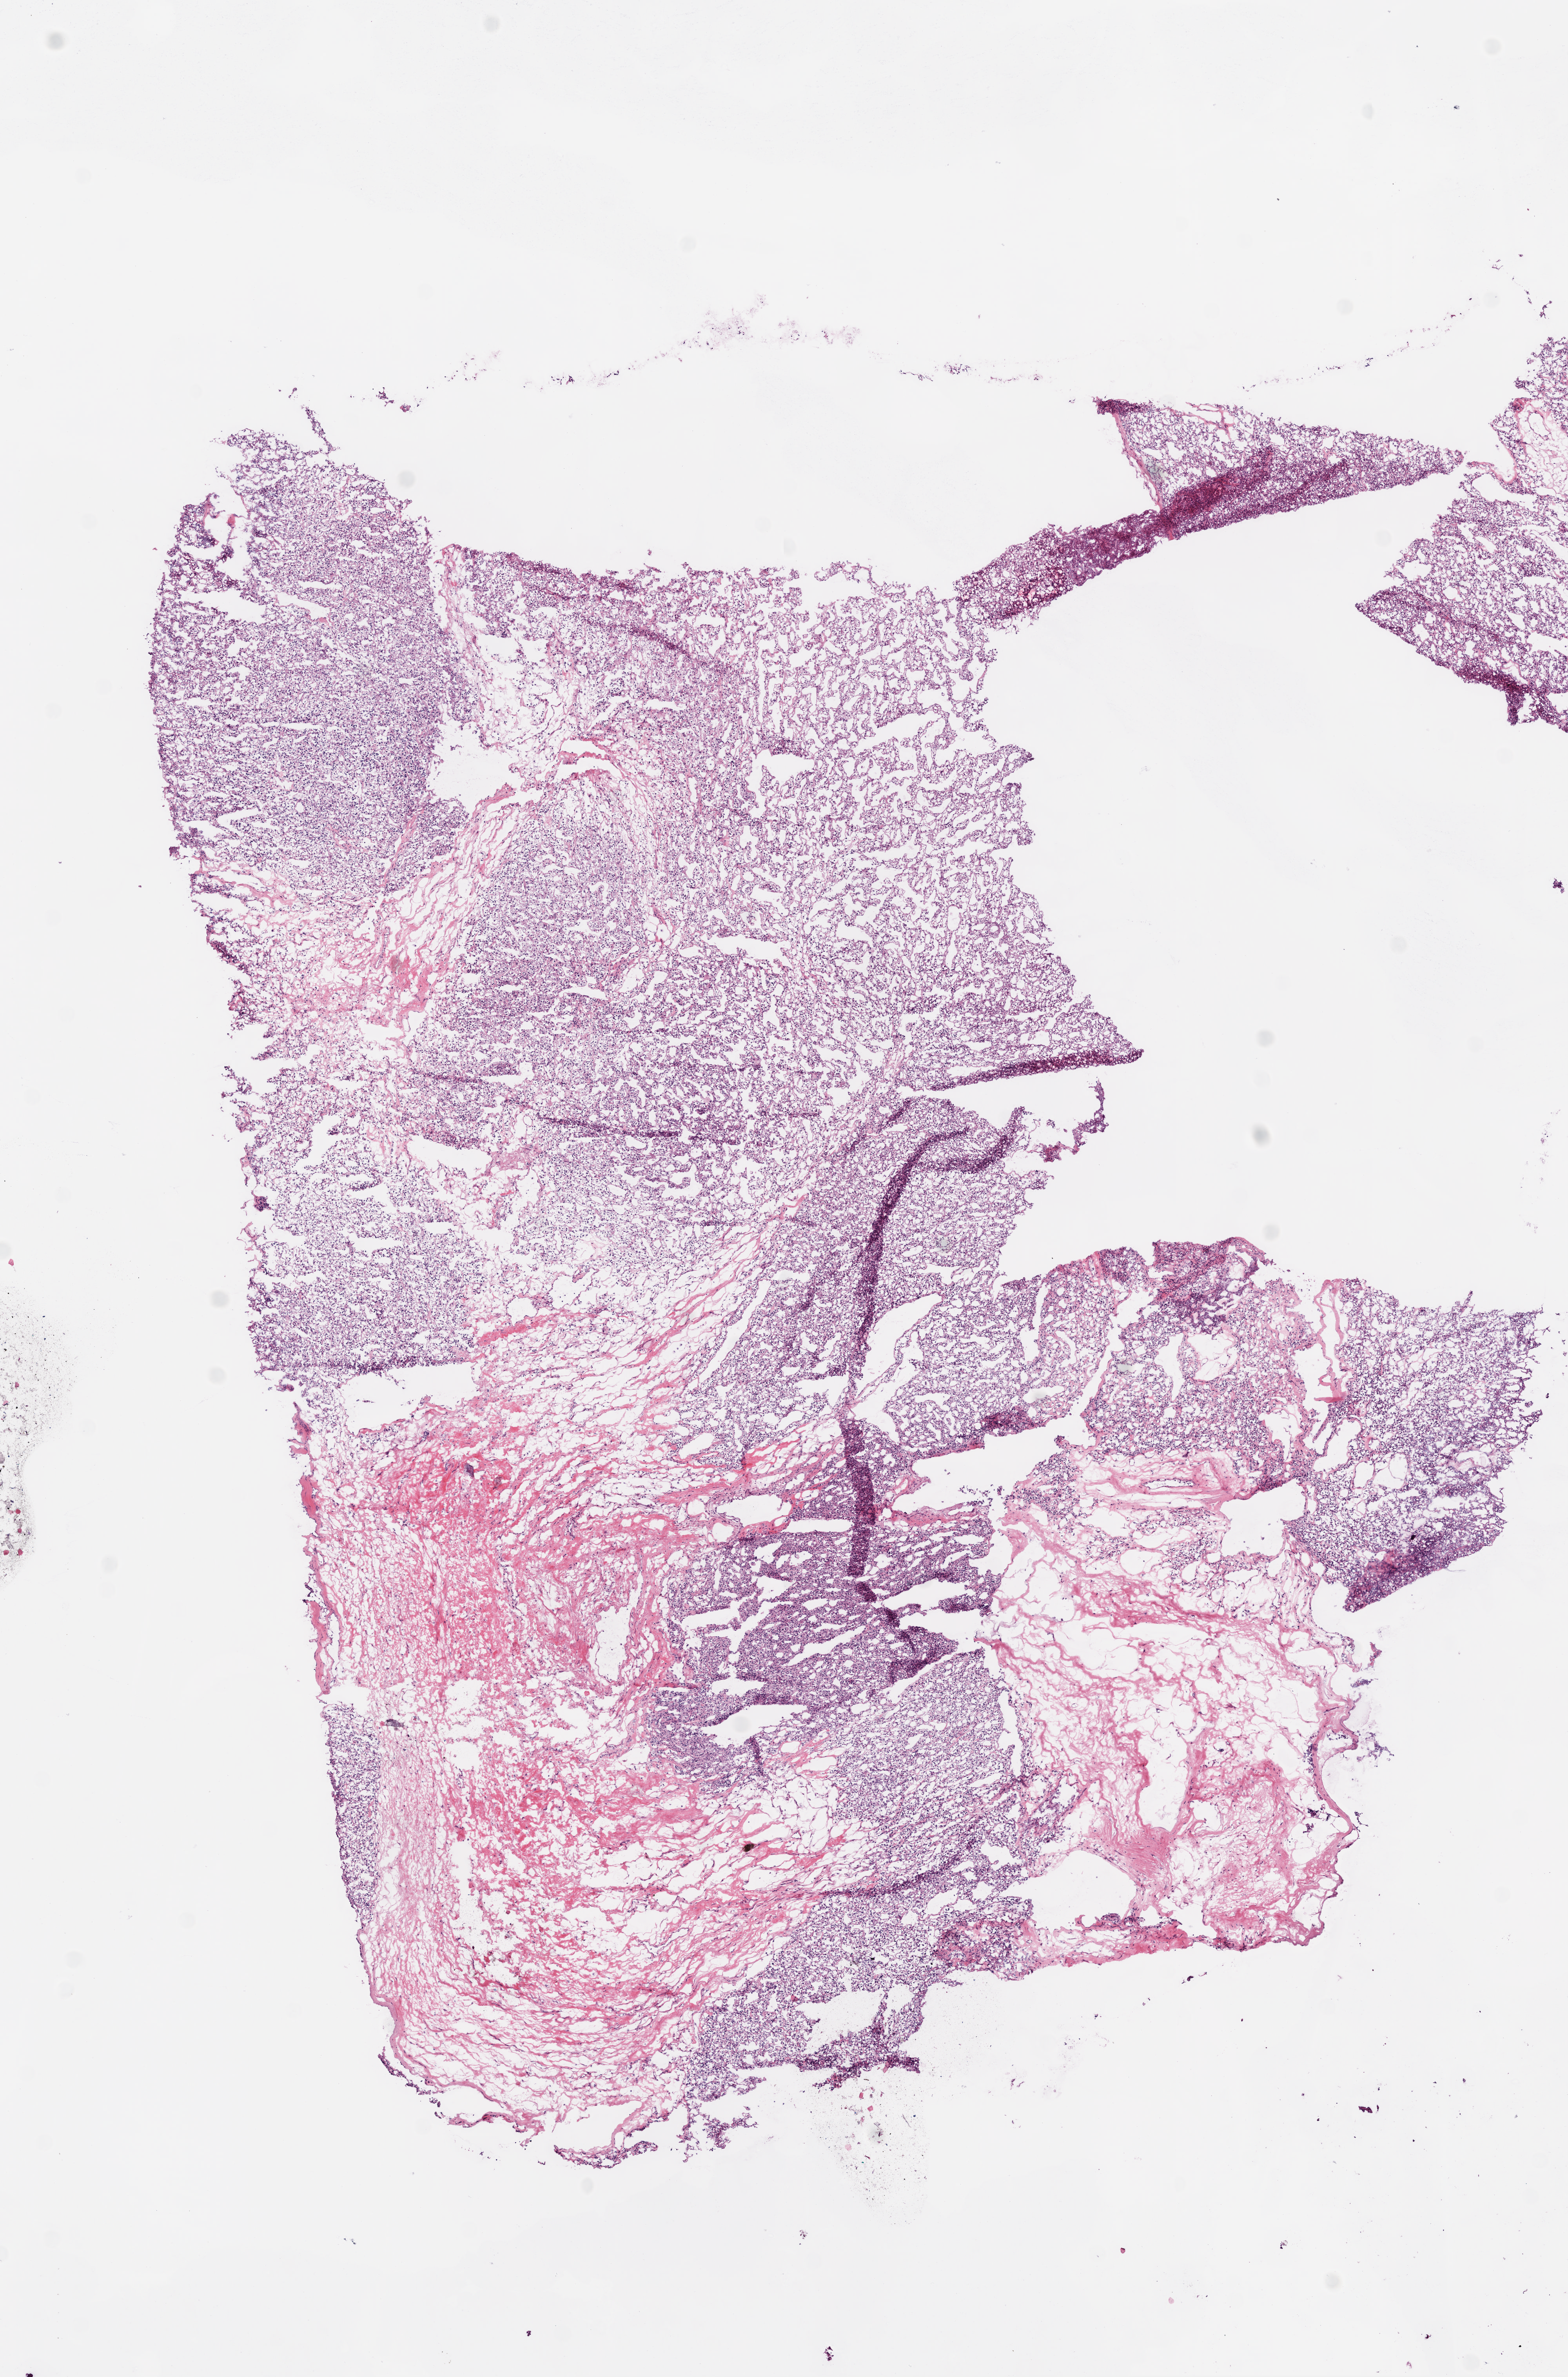
Digitized Hematoxylin and eosin (H&E) stained tissue section (whole slide) — low-resolution overview of the scanned area, about 8.0 x 12.2 mm (slide scanned at 20x); frozen section; kidney, primary tumour sample. Male patient; age at initial diagnosis 72 years. Histologic grade: G2 (moderately differentiated). Pathologist review of this section (percent, as recorded): tumour cells 65%, tumour nuclei 75%, normal cells 0%, stromal cells 35%, necrosis 0%.
Diagnosis: Clear cell adenocarcinoma, NOS. AJCC pathologic stage: I.